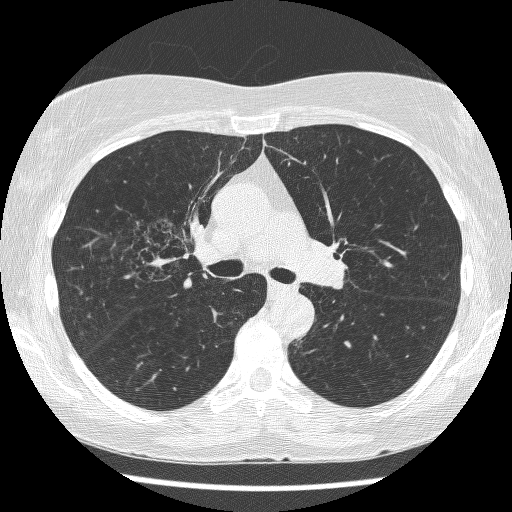
Axial slice from a low-dose chest CT screening exam, baseline screening round, lung window (W 1500 / L -600 HU), slice 173 of 271 in the series, 512 × 512 image matrix. Female, age 64 years at enrolment. Former smoker at enrolment.
- Expert reader's lesion annotation, bounding box <124,220,202,288> (left, top, right, bottom; pixels).
- The screening reader recorded 3 non-calcified nodules or masses ≥4 mm on this exam (right upper lobe, right upper lobe, left lower lobe); which of them this box marks is not recorded.
- Official screen result: positive, change unspecified: nodule(s) >= 4 mm or enlarging nodule(s), mass(es), or other non-specific abnormalities suspicious for lung cancer.
- Lung cancer was diagnosed 735 days after this screen: adenocarcinoma, NOS, right upper lobe, right middle lobe, right hilum, stage IV (AJCC 6th edition), 85 mm at pathology.